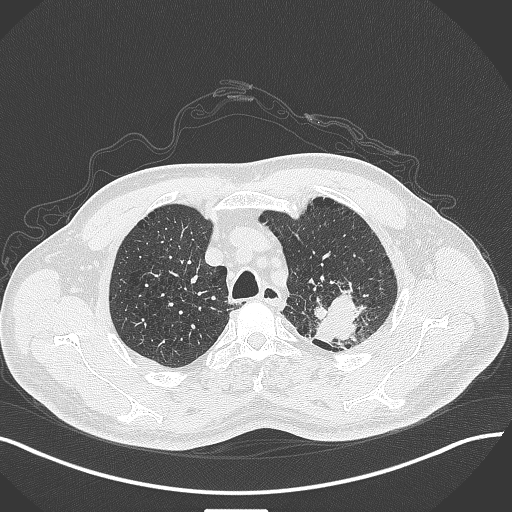
Chest CT, one axial slice. Slice 341 of 429 in the series (ordered by position). Reconstruction kernel B70f. Lung window (W 1500 / L -600 HU). 512 × 512 image matrix, field of view 400 × 400 mm. Male patient, age 55 years. Case-level facts recorded for this patient, not image findings: clinical TNM (as recorded): T3 N0 M1c.
Structures marked on this image (bounding box drawn by a radiologist):
- lung tumour (recorded histology: adenocarcinoma): bounding box (x1, y1, x2, y2) in pixels: (308, 289, 376, 352)